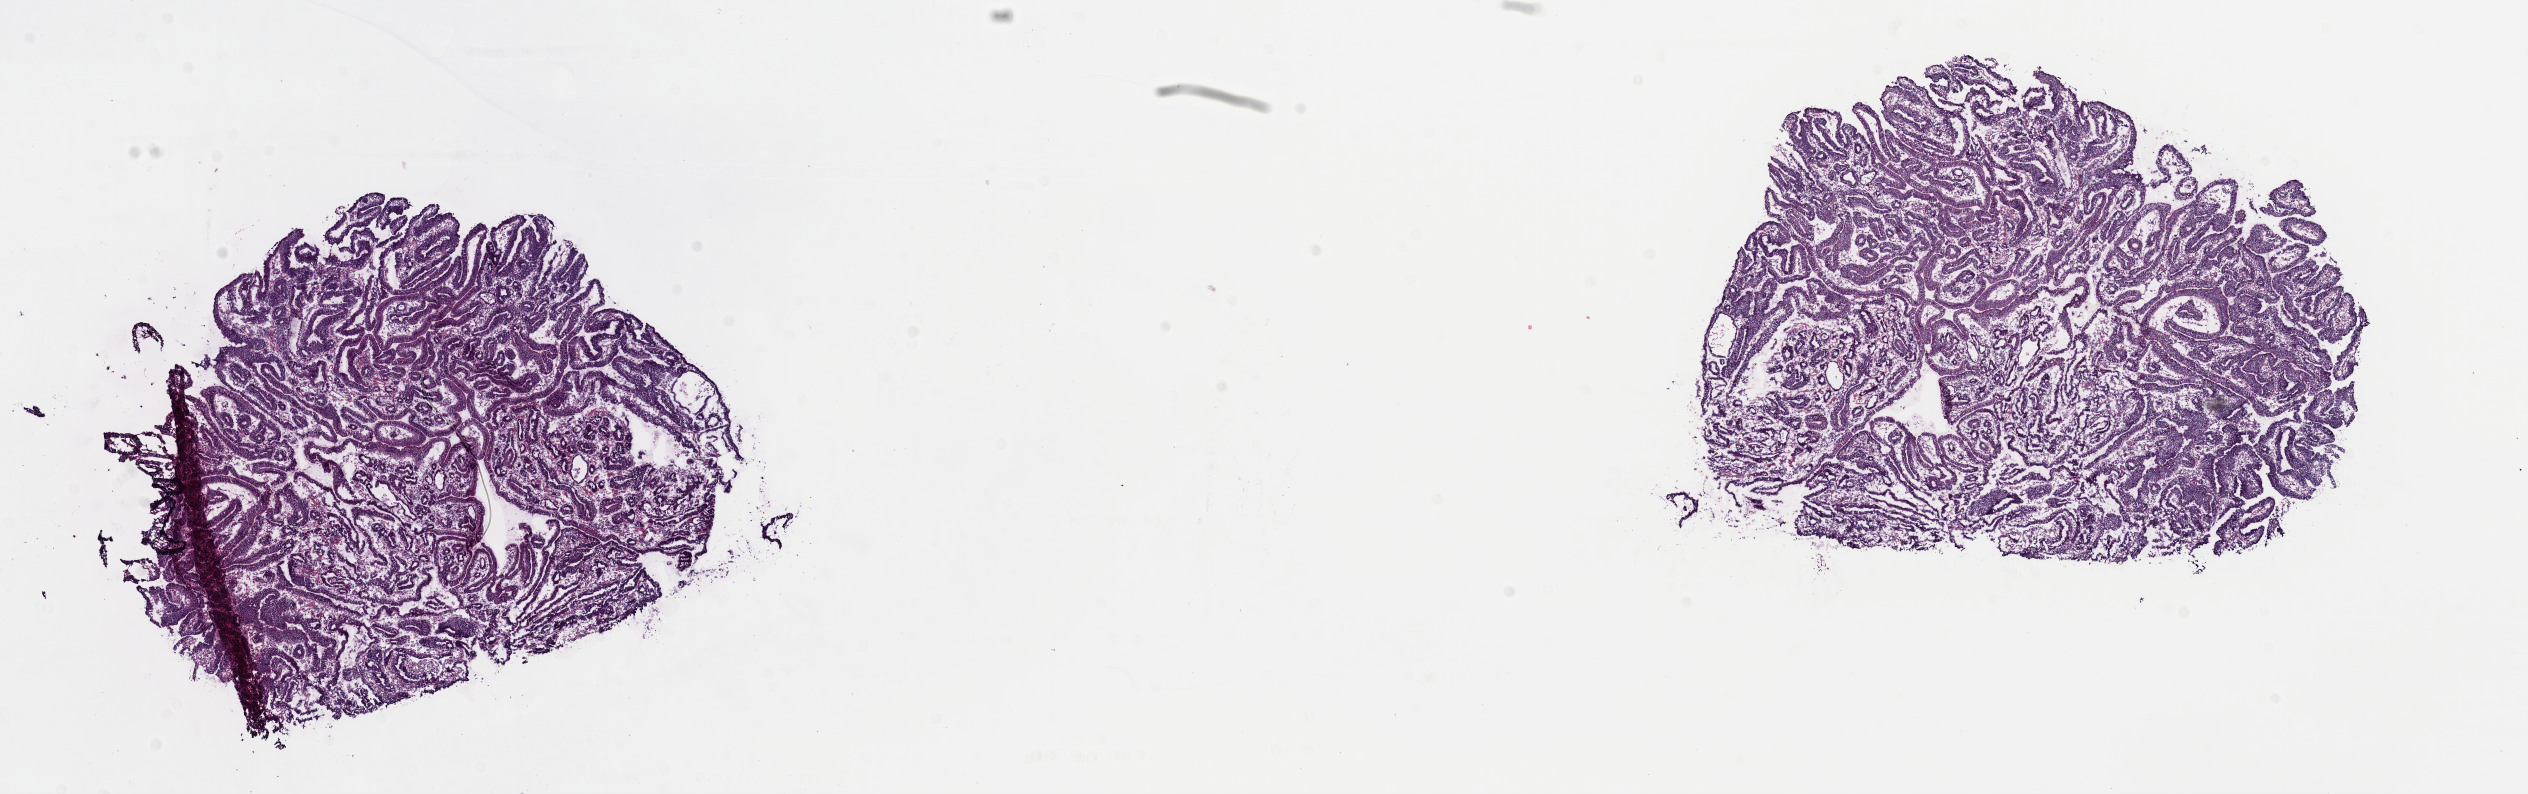
Digitized H&E tissue section (whole slide) — shown as a low-resolution overview of the whole scanned area (about 20.0 x 6.3 mm, acquisition: 40x scan), frozen section, sample: primary tumour, stomach. Patient: female, age at initial diagnosis 67 years. Histologic grade: G2 (moderately differentiated). Slide review estimates, as recorded: tumour cells 94%, tumour nuclei 85%, normal cells 0%, stromal cells 5%, necrosis 1%. Inflammatory infiltration, as recorded: lymphocyte infiltration 2%, monocyte infiltration 1%, neutrophil infiltration 0%.
• pathologic diagnosis: Tubular adenocarcinoma
• AJCC pathologic stage: IA
• lymph nodes positive (case pathology): 0 of 42 examined